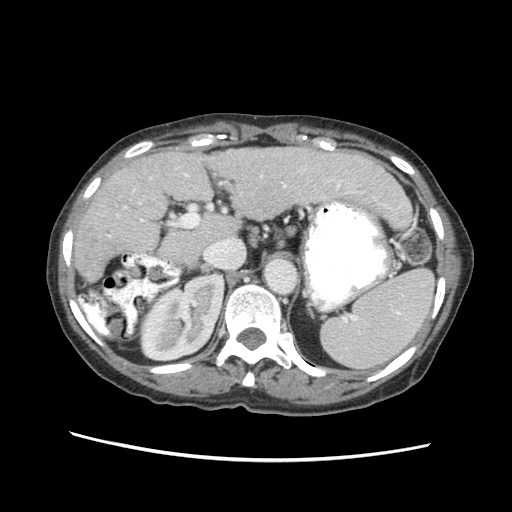
Contrast-enhanced abdominal CT (liver protocol), one axial slice. Slice 36 of 63 in the series (ordered by position). Reconstruction kernel STANDARD. 120 kVp. Soft-tissue window (W 400 / L 40 HU). 512 × 512 image matrix, field of view 340 × 340 mm. From the clinical record (not read from this slice): diagnosis: hepatocellular carcinoma (patient treated with transarterial chemoembolisation; whether this scan precedes or follows treatment is not stated here); TNM stage (as recorded): Stage-I.
Annotated regions visible in this slice (semi-automatically segmented with operator editing):
- abdominal aorta: bounding box (x1, y1, x2, y2) in pixels: (266, 258, 296, 293)
- liver parenchyma outside the tumour (the mass and vessels are separate outlines, so this box may not span the whole liver): (74, 144, 408, 282)
- liver vessels: (123, 172, 361, 220)